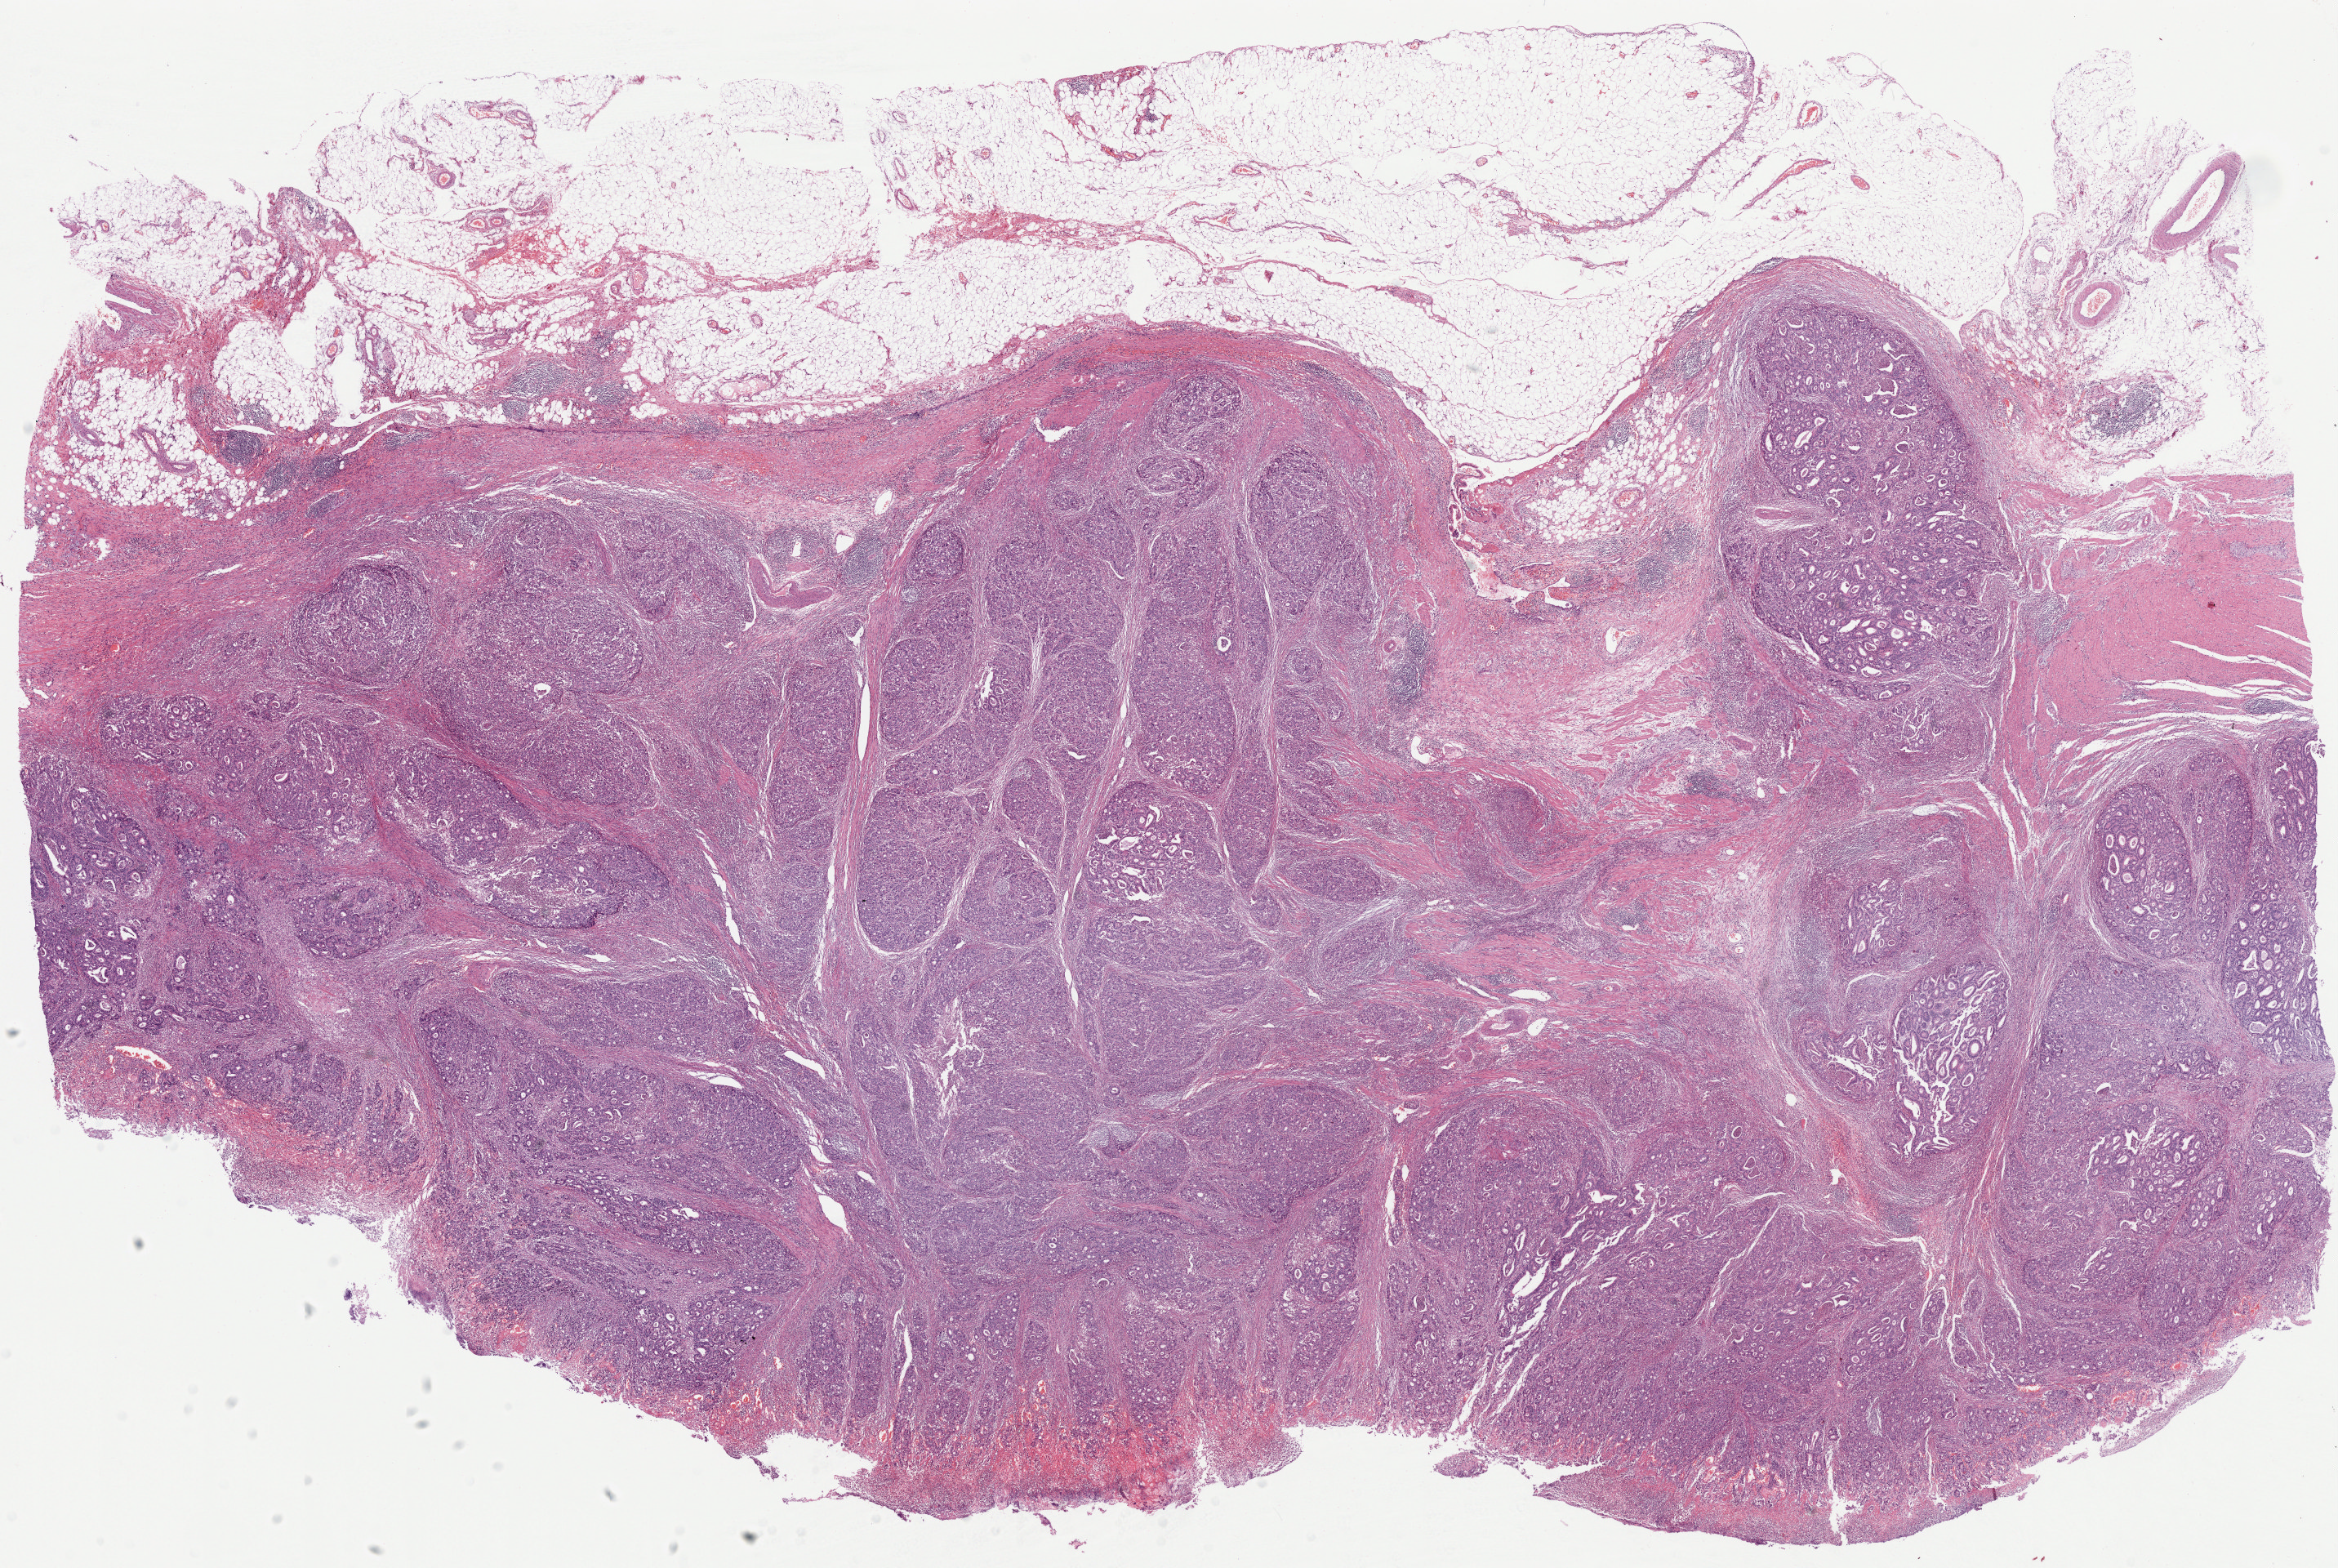
Hematoxylin and eosin (H&E) stained whole-slide image — low-resolution overview of the scanned area, about 22.6 x 15.2 mm (acquisition: 20x scan), FFPE section, primary tumour sample from the stomach. Female patient; age at initial diagnosis 82 years. Histologic grade: G2 (moderately differentiated).
Diagnosis: Tubular adenocarcinoma. AJCC pathologic stage: IIA (7th edition). Lymph nodes positive (case pathology): 0 of 27 examined.